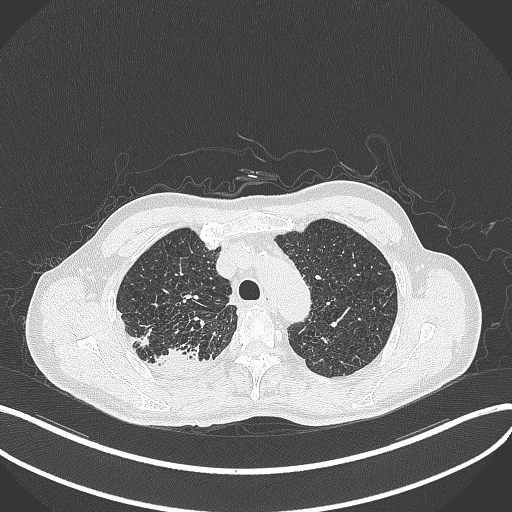
Chest CT, one axial slice. Position 347 of 428 along the scan axis. 120 kVp. Lung window (W 1500 / L -600 HU). 1 mm slice thickness. 512 × 512 image matrix, field of view 400 × 400 mm. Male patient, age 79 years. Case-level facts recorded for this patient, not image findings: clinical TNM (as recorded): T3 N0 M0.
Structures marked on this image (rectangle marked by the reading radiologist):
- lung tumour (recorded histology: adenocarcinoma): bounding box <153,343,216,379> (left, top, right, bottom; pixels)